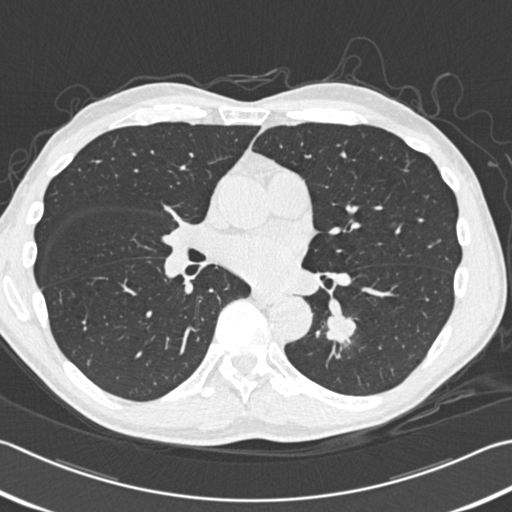
Low-dose screening chest CT, one axial slice. Reconstruction kernel B30f. Lung window (W 1500 / L -600 HU). 1 mm slice thickness. 512 × 512 image matrix.
Annotated regions visible in this slice (outlined manually by an expert reader):
- lesion 1 (tumor, lower lobe of left lung): box from (x=327, y=315) to (x=356, y=344) px